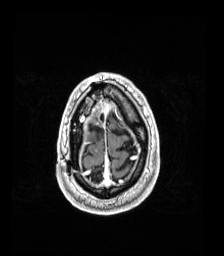
Brain MRI from a brain-tumour surgery series, one axial slice; T1-weighted post-contrast; 1 mm slice thickness; 224 × 256 image matrix, field of view 224 × 256 mm. From the clinical record (not read from this slice): histopathology: Astrocytoma; WHO grade: 4; IDH mutation: yes; tumour location: Right Frontal.
Outlined on this slice (outlined manually by an expert reader):
- previous resection cavity: bounding box [x1, y1, x2, y2] px = [90, 124, 103, 133]